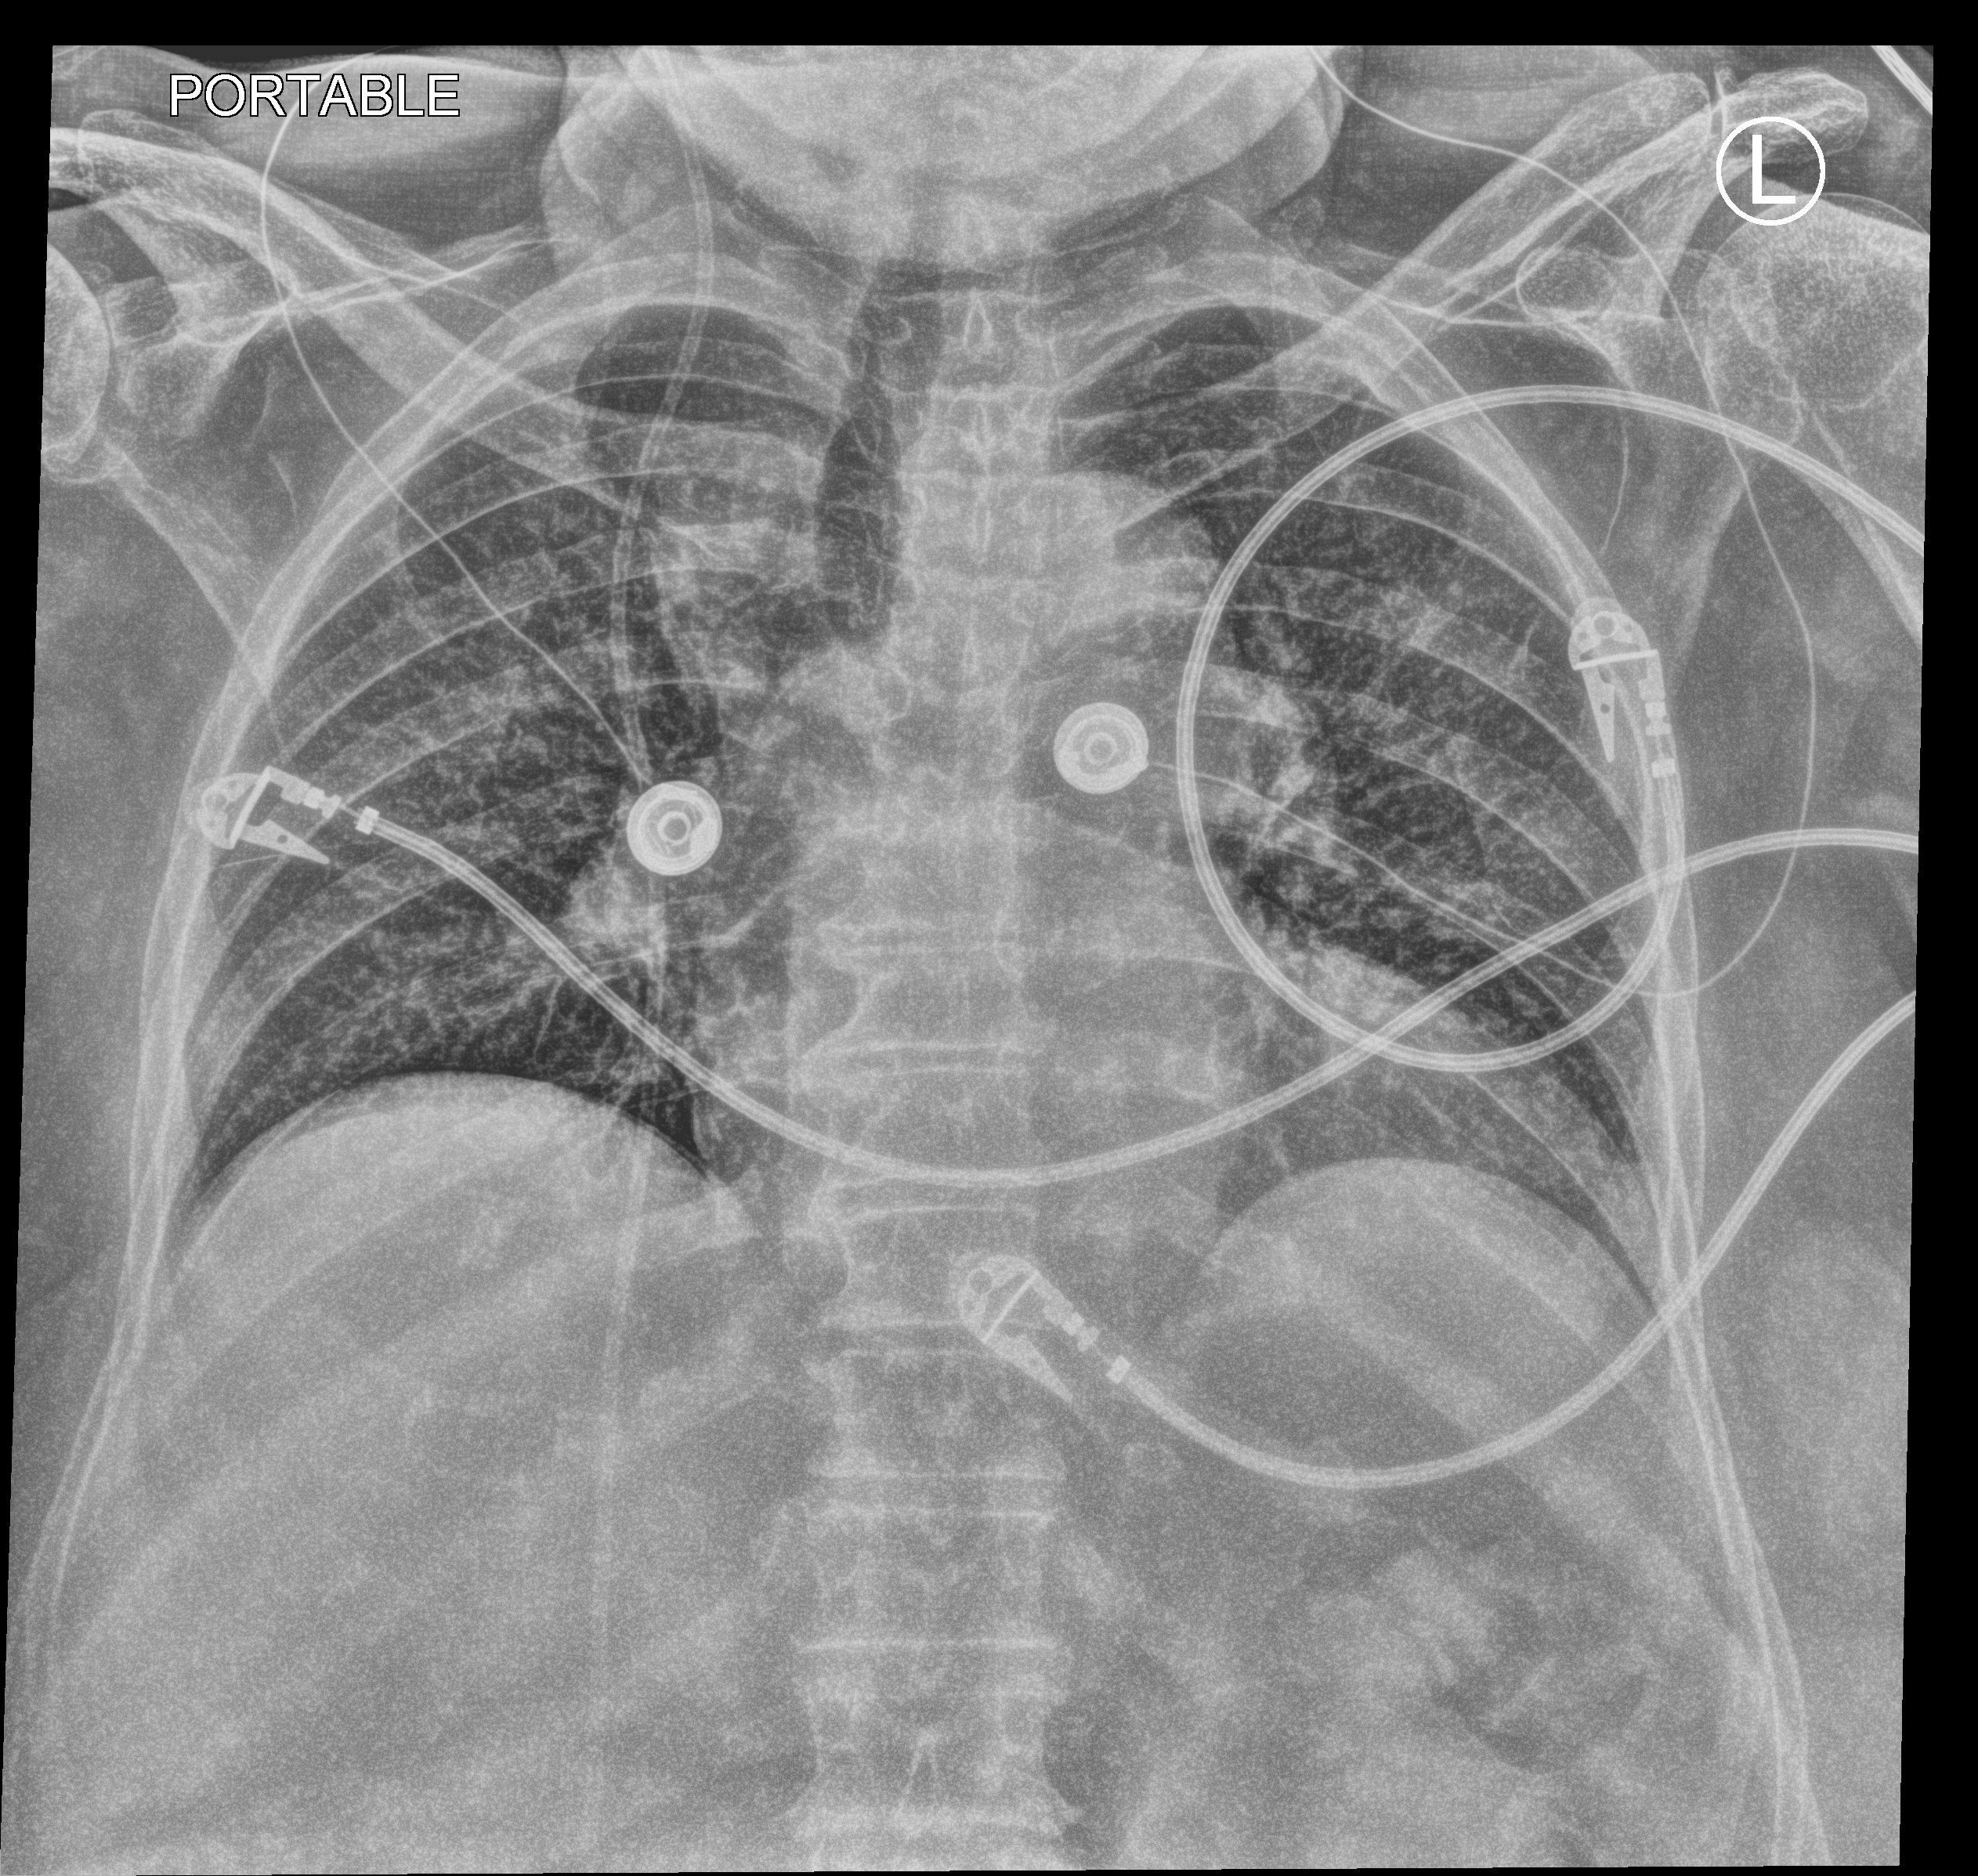
Bedside chest radiograph (computed radiography). Female patient hospitalised with COVID-19, age 75–90 years.
From the hospital-stay record, not from the radiograph (when in the stay this image was taken is not recorded): admitted to intensive care during this hospital stay: yes.